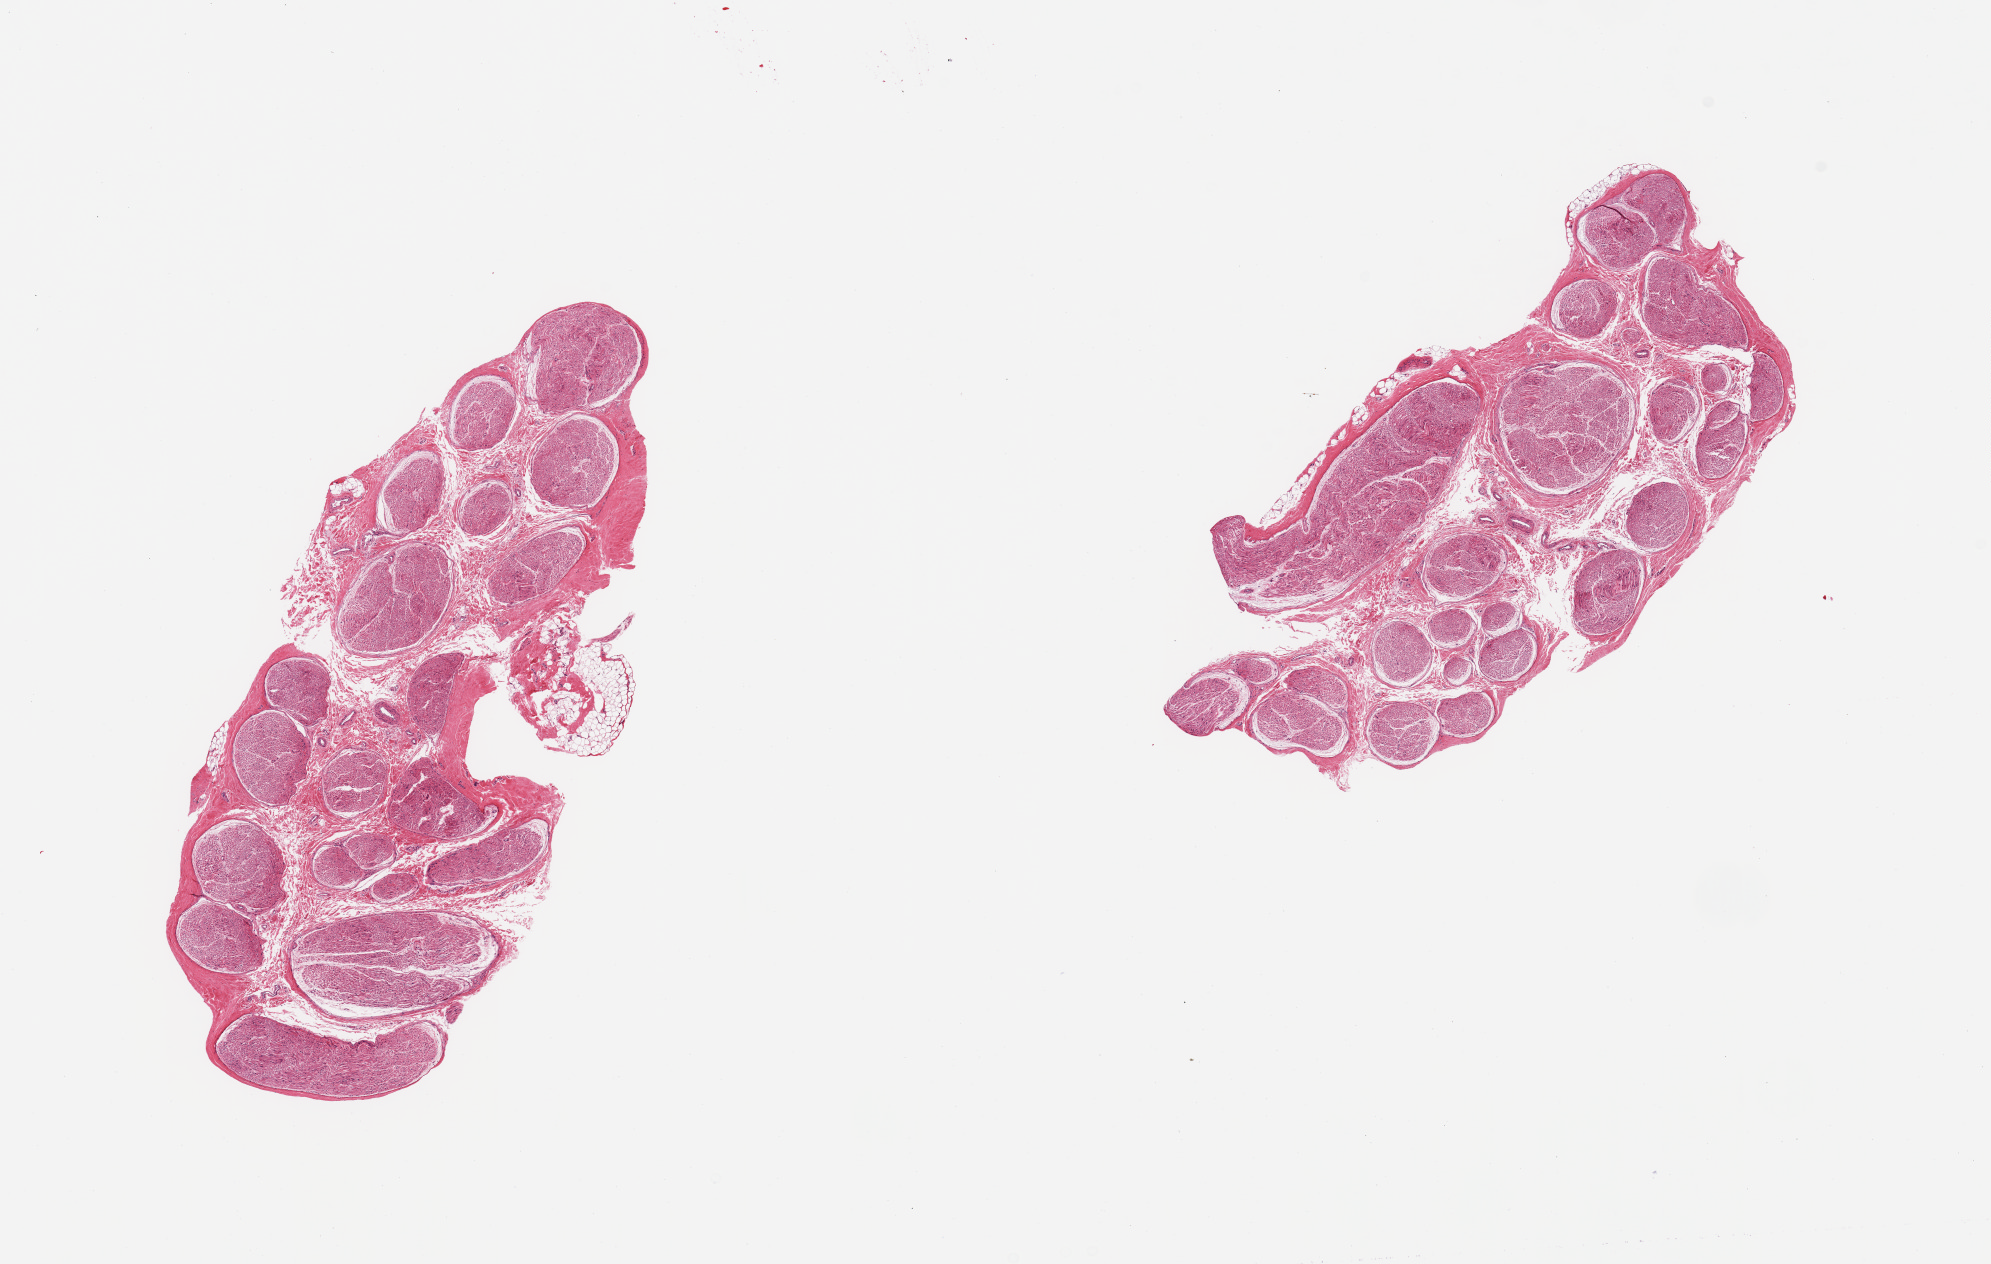
Hematoxylin and eosin (H&E) whole-slide image, brightfield, whole scanned area (about 15.8 x 10.0 mm, acquisition: 20x scan) shown as a low-resolution overview. PAXgene-fixed, paraffin-embedded tissue. Section of tibial nerve (target tissue). Donor tissue sample. Donor: male.
* pathologist's review note for this sample: 2 pieces; <10% attached fat